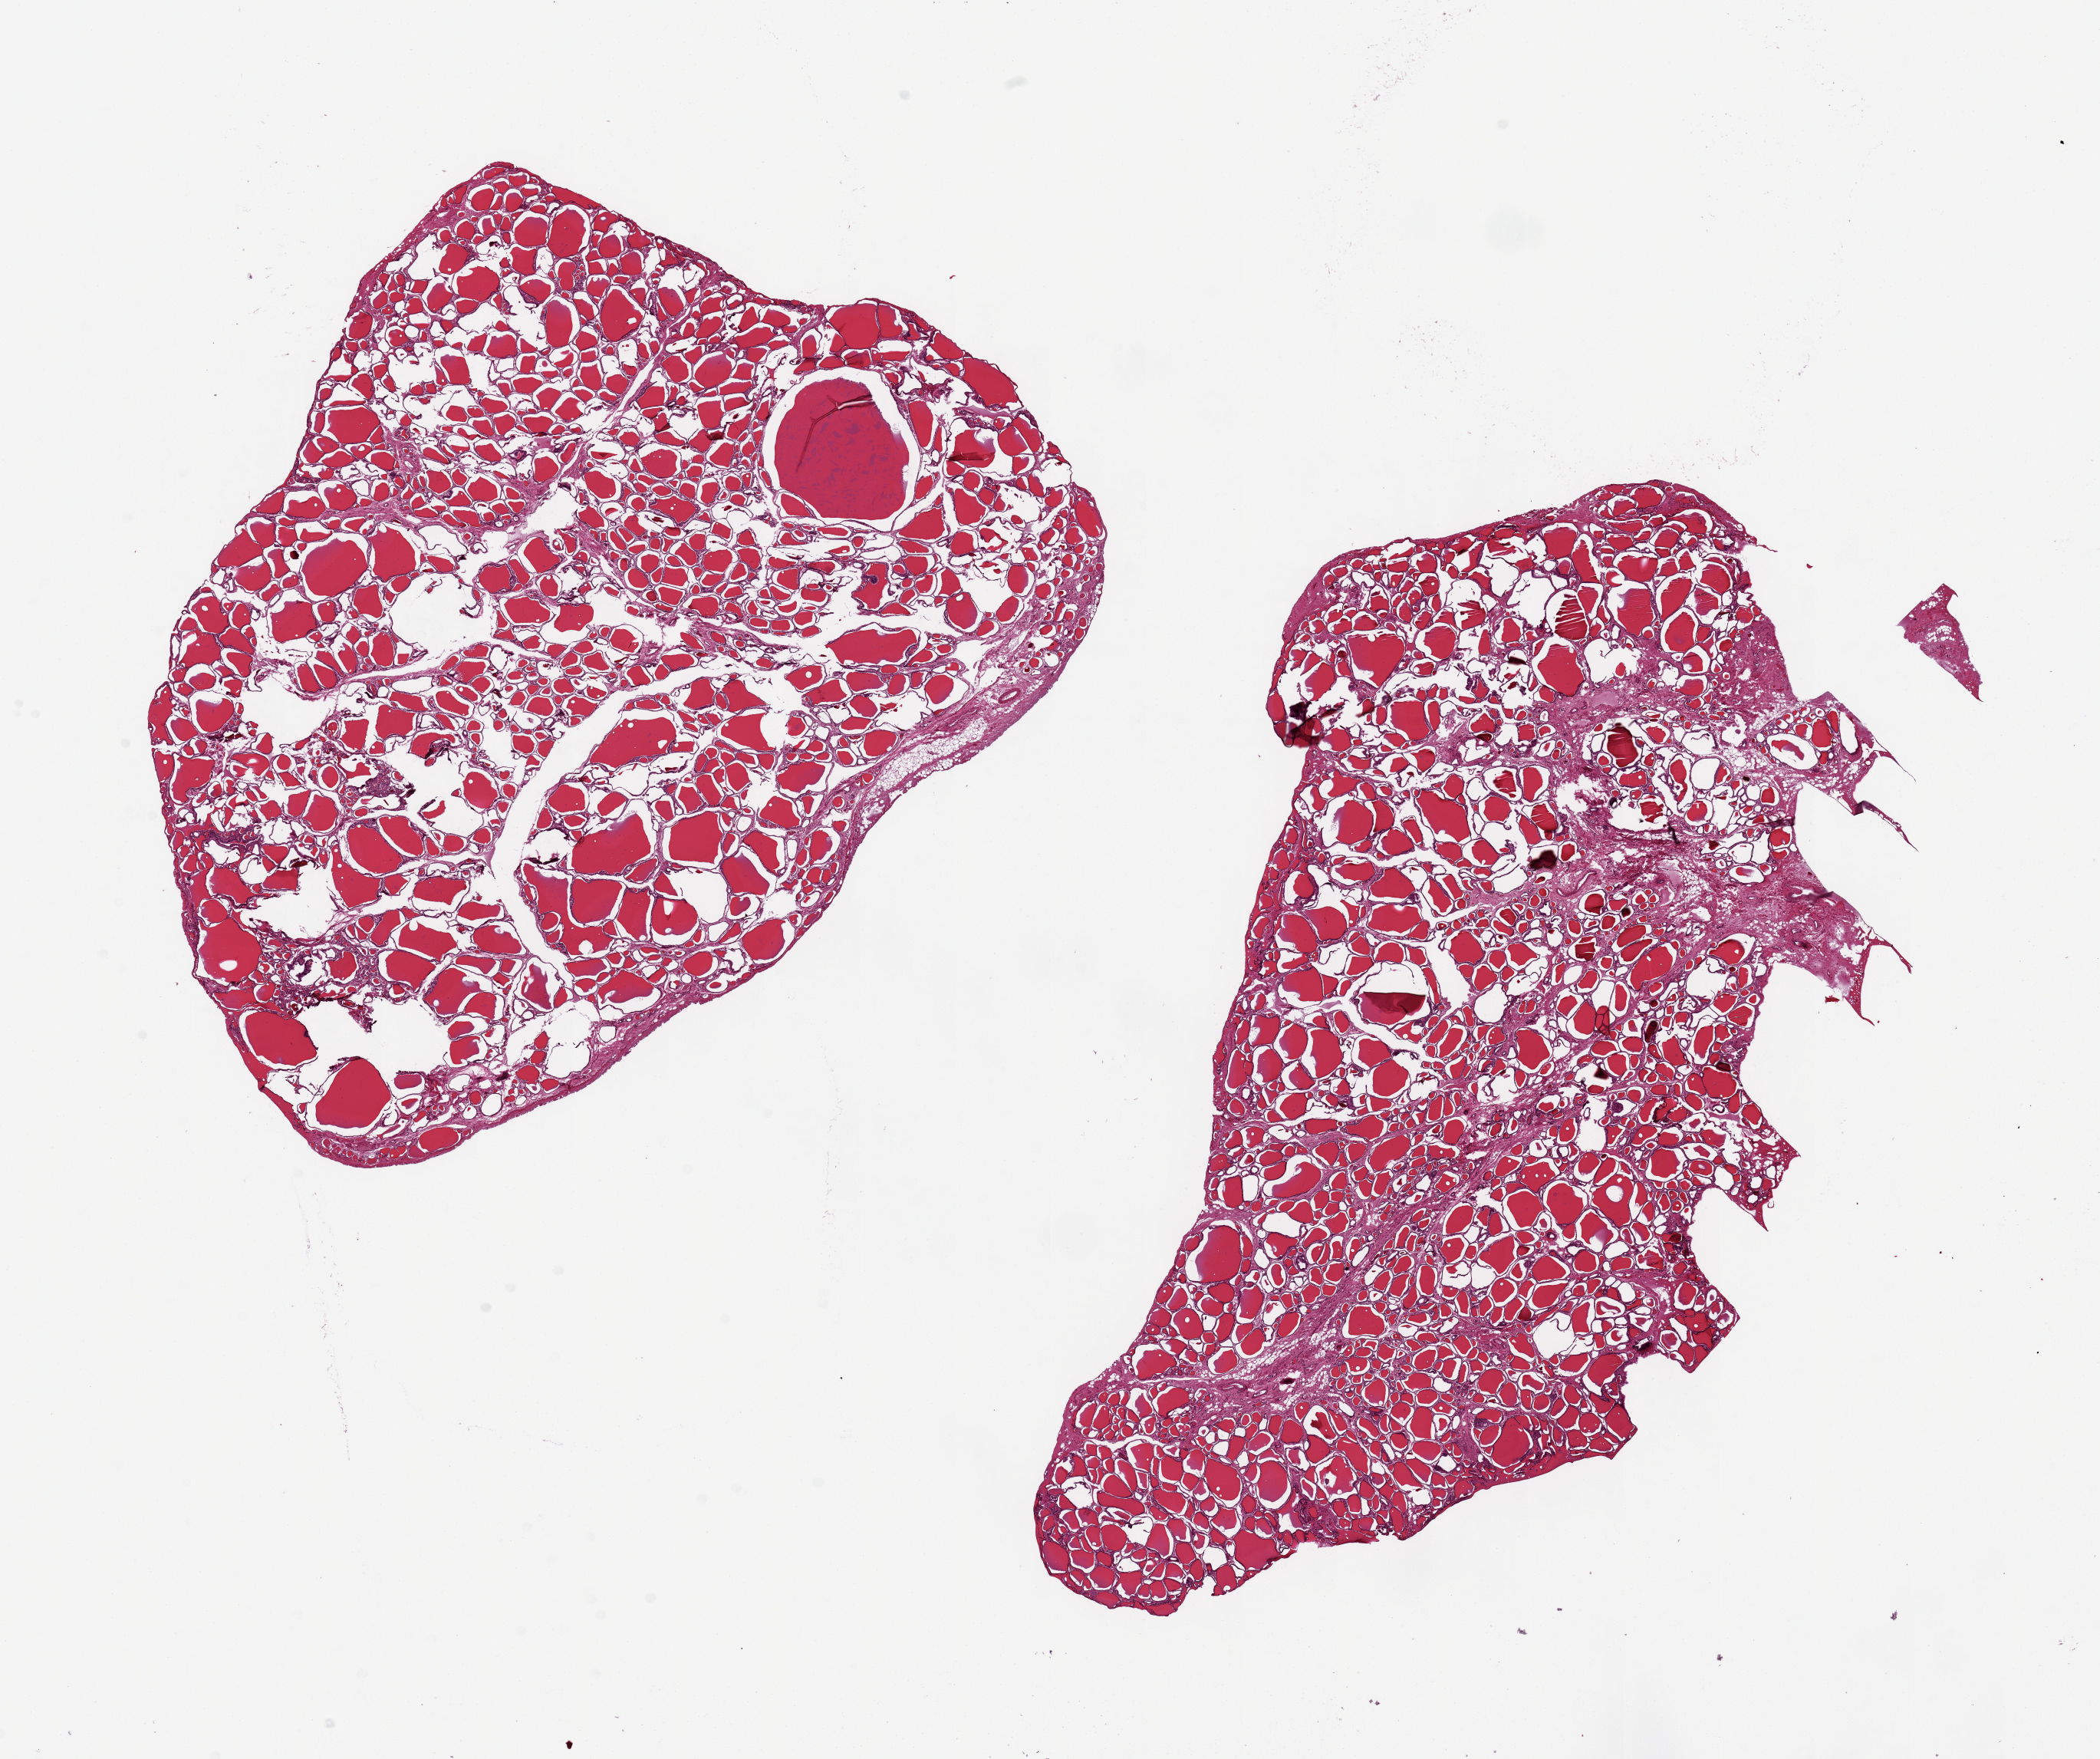
Digitized haematoxylin and eosin-stained section, brightfield — a low-resolution overview of the entire scanned area, about 21.7 x 18.1 mm; PAXgene-fixed paraffin-embedded (PFPE) section; section of thyroid (target tissue); tissue donor sample. Donor: male.
- review note (as recorded): 2 pieces, 10.5x8 & 13x7 mm